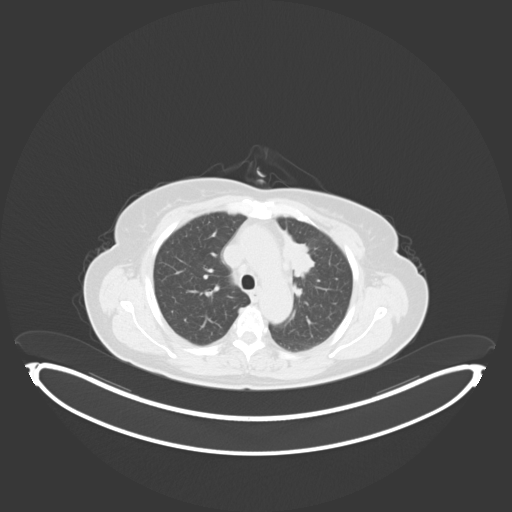
Chest CT, one axial slice; position 192 of 243 along the scan axis; reconstruction kernel B30f; lung window (W 1500 / L -600 HU); 512 × 512 image matrix, field of view 500 × 500 mm. Female patient, age 65 years. From the clinical record (not read from this slice): clinical TNM (as recorded): T2a N0 M0.
Outlined on this slice (rectangle marked by the reading radiologist):
- lung tumour (recorded histology: adenocarcinoma): bounding box <281,229,316,280> (left, top, right, bottom; pixels)